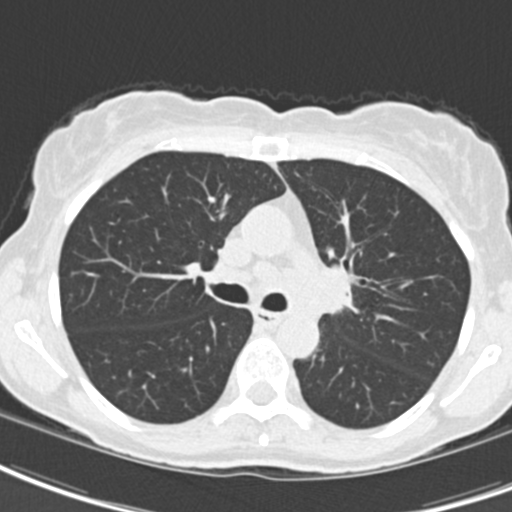
Low-dose screening chest CT, one axial slice. Slice 128 of 189 in the series (ordered by position). 120 kVp. Lung window (W 1500 / L -600 HU). 2 mm slice thickness. 512 × 512 image matrix, field of view 279 × 279 mm.
Structures marked on this image (outlined manually by an expert reader):
- lesion 2 (tumor, hilum of left lung): box from (x=319, y=267) to (x=350, y=312) px